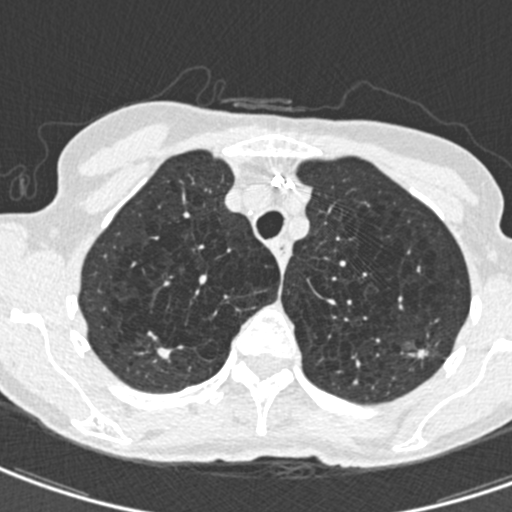
Chest CT (low-dose screening protocol), one axial image; second annual screen; lung window (W 1500 / L -600 HU); 120 kVp; slice 111 of 498 in the series; 512 × 512 image matrix. Female, age 71 years at enrolment. Current smoker at enrolment.
- Expert-annotated lung lesion, bounding box <405,332,445,370> (left, top, right, bottom; pixels).
- The screening reader recorded 2 non-calcified nodules or masses ≥4 mm on this exam; which of them this box marks is not recorded.
- Later outcome: lung cancer diagnosed 604 days after this screen — adenocarcinoma, NOS, left upper lobe, moderately differentiated (G2), stage IA (AJCC 6th edition), 12 mm at pathology.